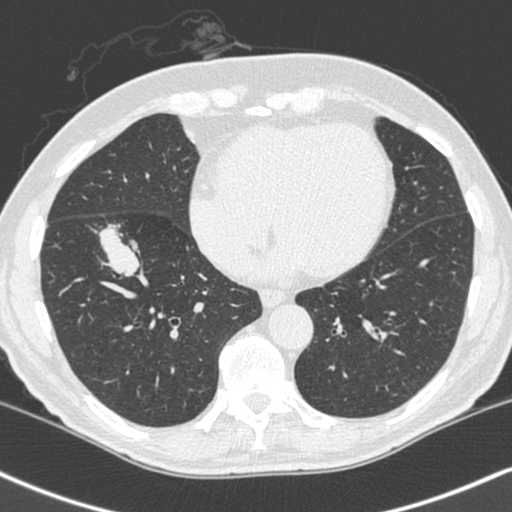
Low-dose screening chest CT, axial slice, baseline annual screen, lung window (W 1500 / L -600 HU), standard (soft-tissue) reconstruction kernel (C), slice 151 of 248 in the series, 512 × 512 image matrix. Male participant, aged 68 years at enrolment.
Lesion marked by an expert reader, bounding box [x1, y1, x2, y2] px = [83, 214, 158, 284]. Screening reader's record for this exam (one nodule recorded; not confirmed to be the boxed lesion): non-calcified nodule or mass ≥4 mm, right lower lobe, 34 × 17 mm, smooth margins, soft tissue attenuation. Later outcome: lung cancer diagnosed 24 days after this screen — combined small cell carcinoma, right lower lobe, stage IIIA (AJCC 6th edition), 41 mm at pathology.